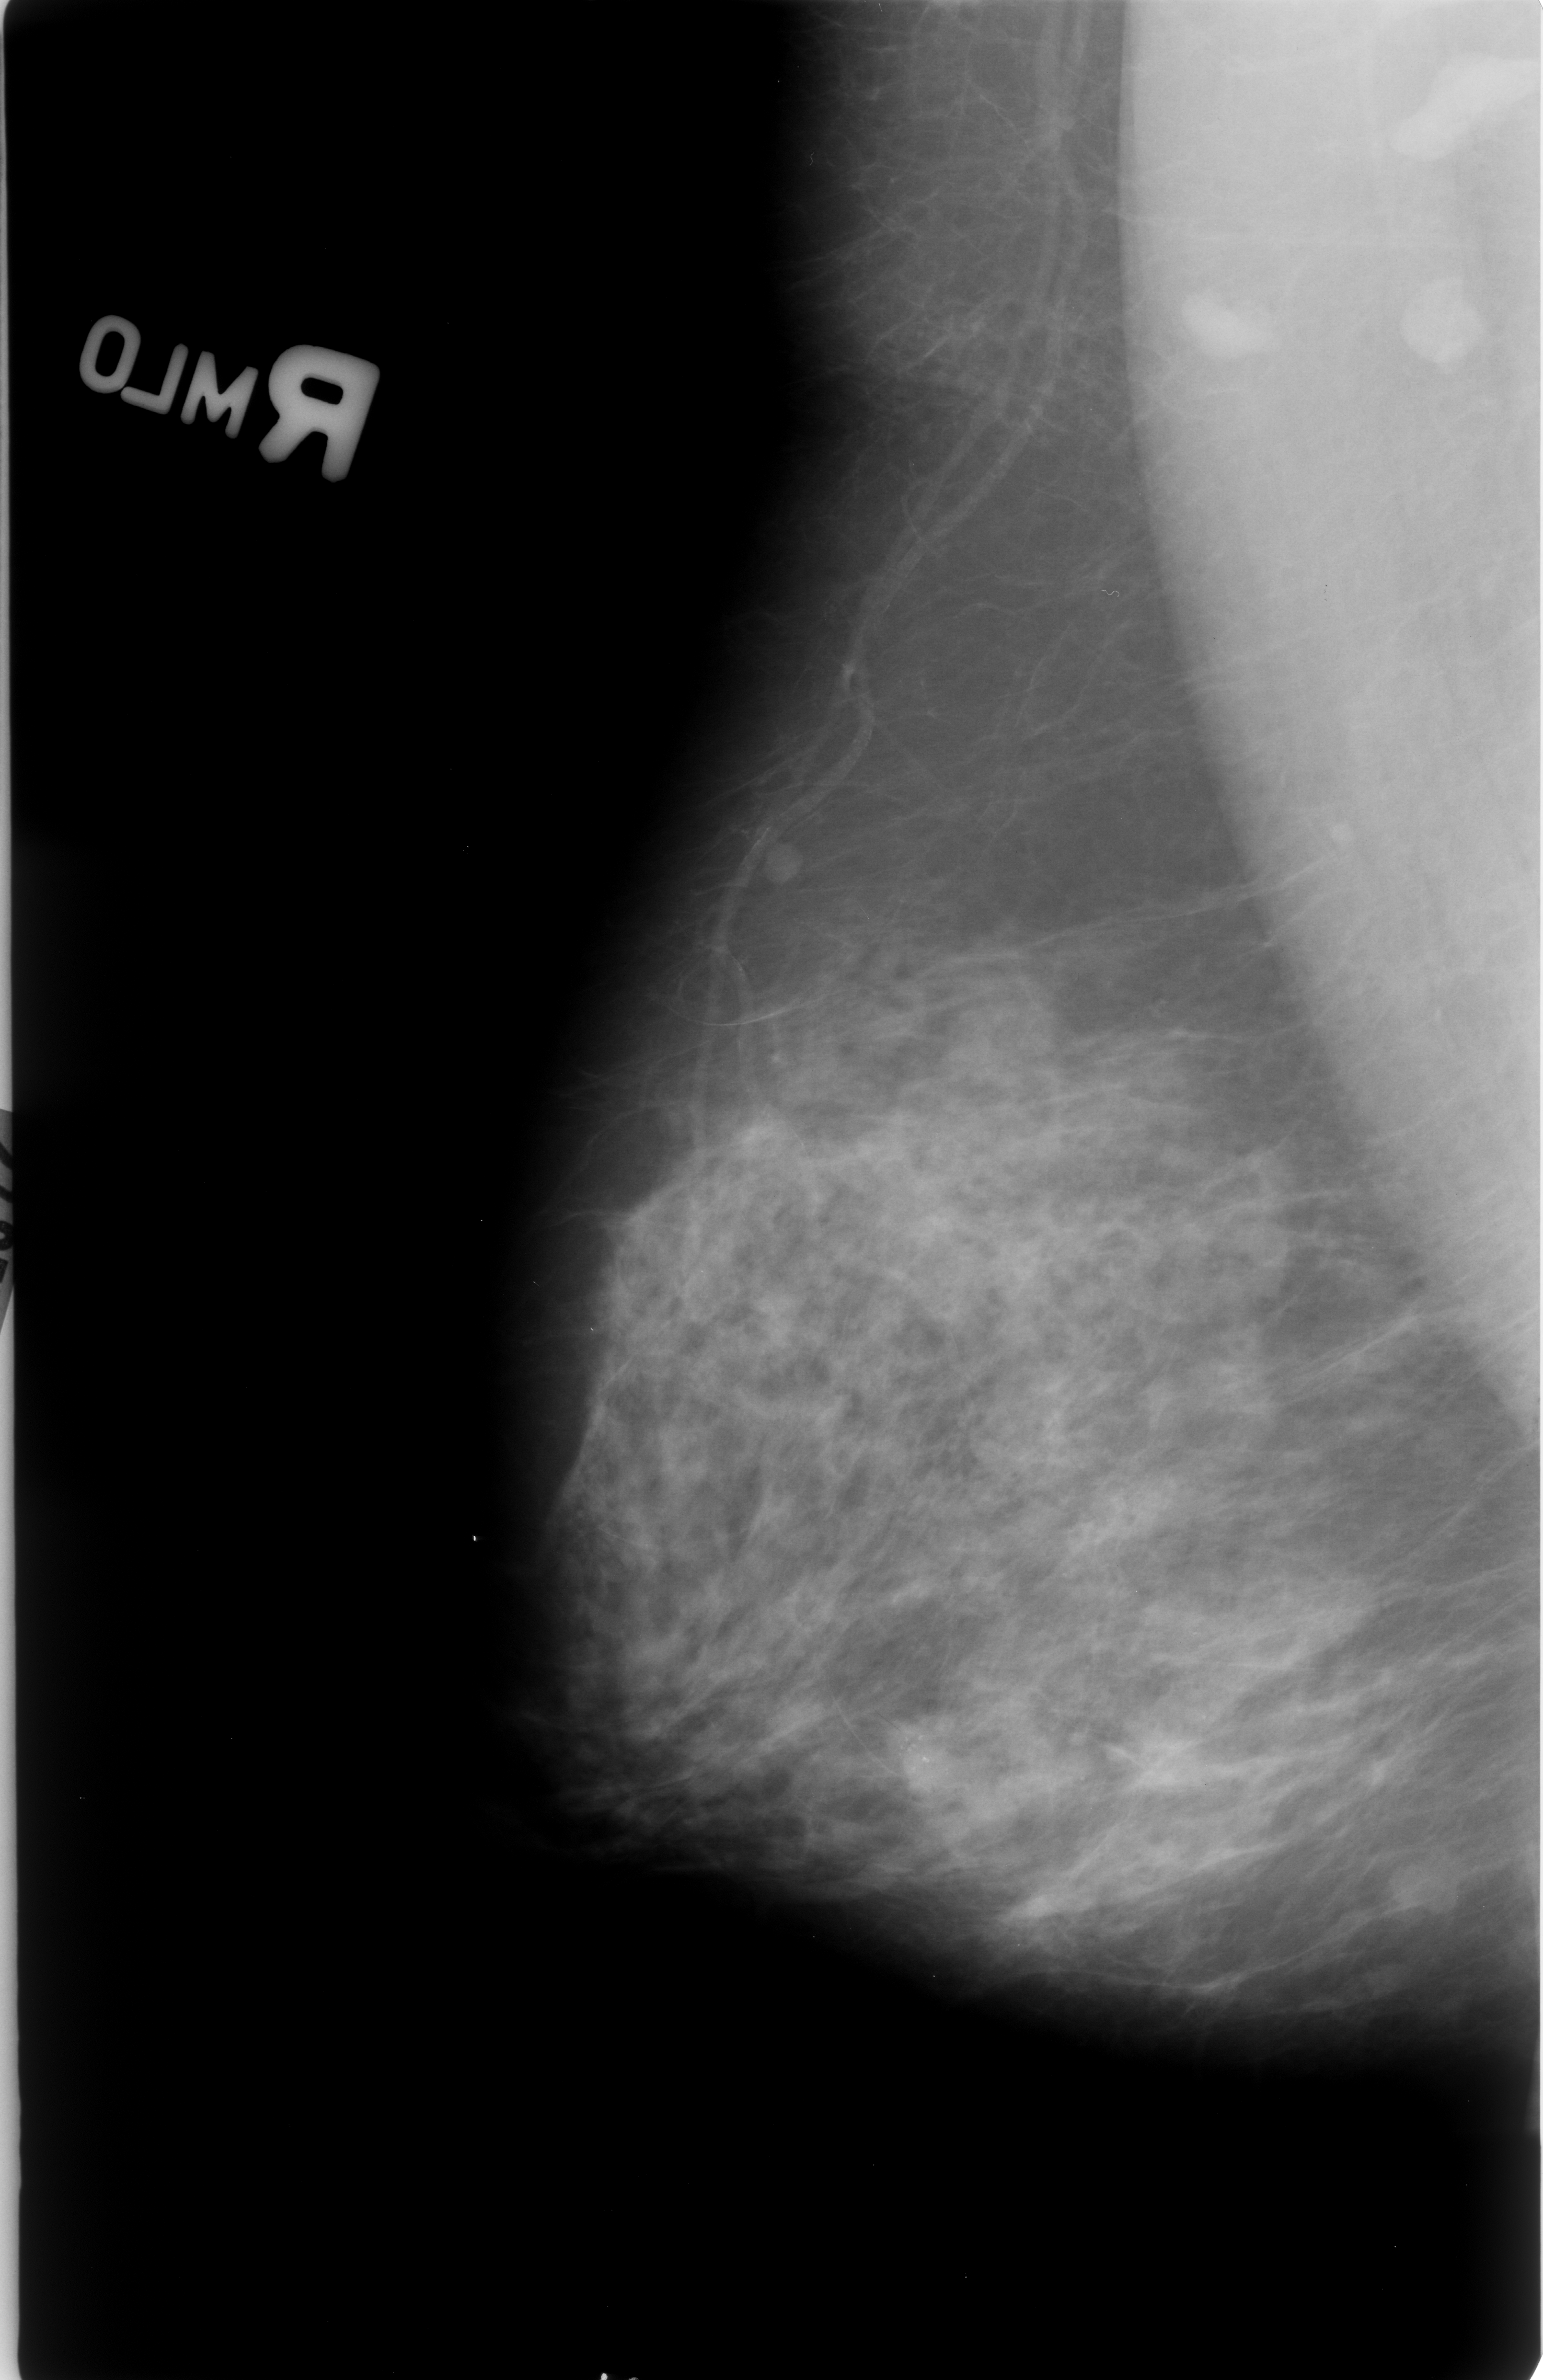
Digitized screen-film mammogram. Right breast. MLO view. BI-RADS breast density category 3 (scale 1–4). 1543 × 2380 image matrix.
Expert-marked regions of interest on this image (one box per marked abnormality):
- calcifications, morphology pleomorphic, distribution clustered; BI-RADS assessment category 4; subtlety rating 3 on a 1 (subtle) to 5 (obvious) scale; pathology (as recorded): malignant: box from (x=882, y=1706) to (x=971, y=1812) px